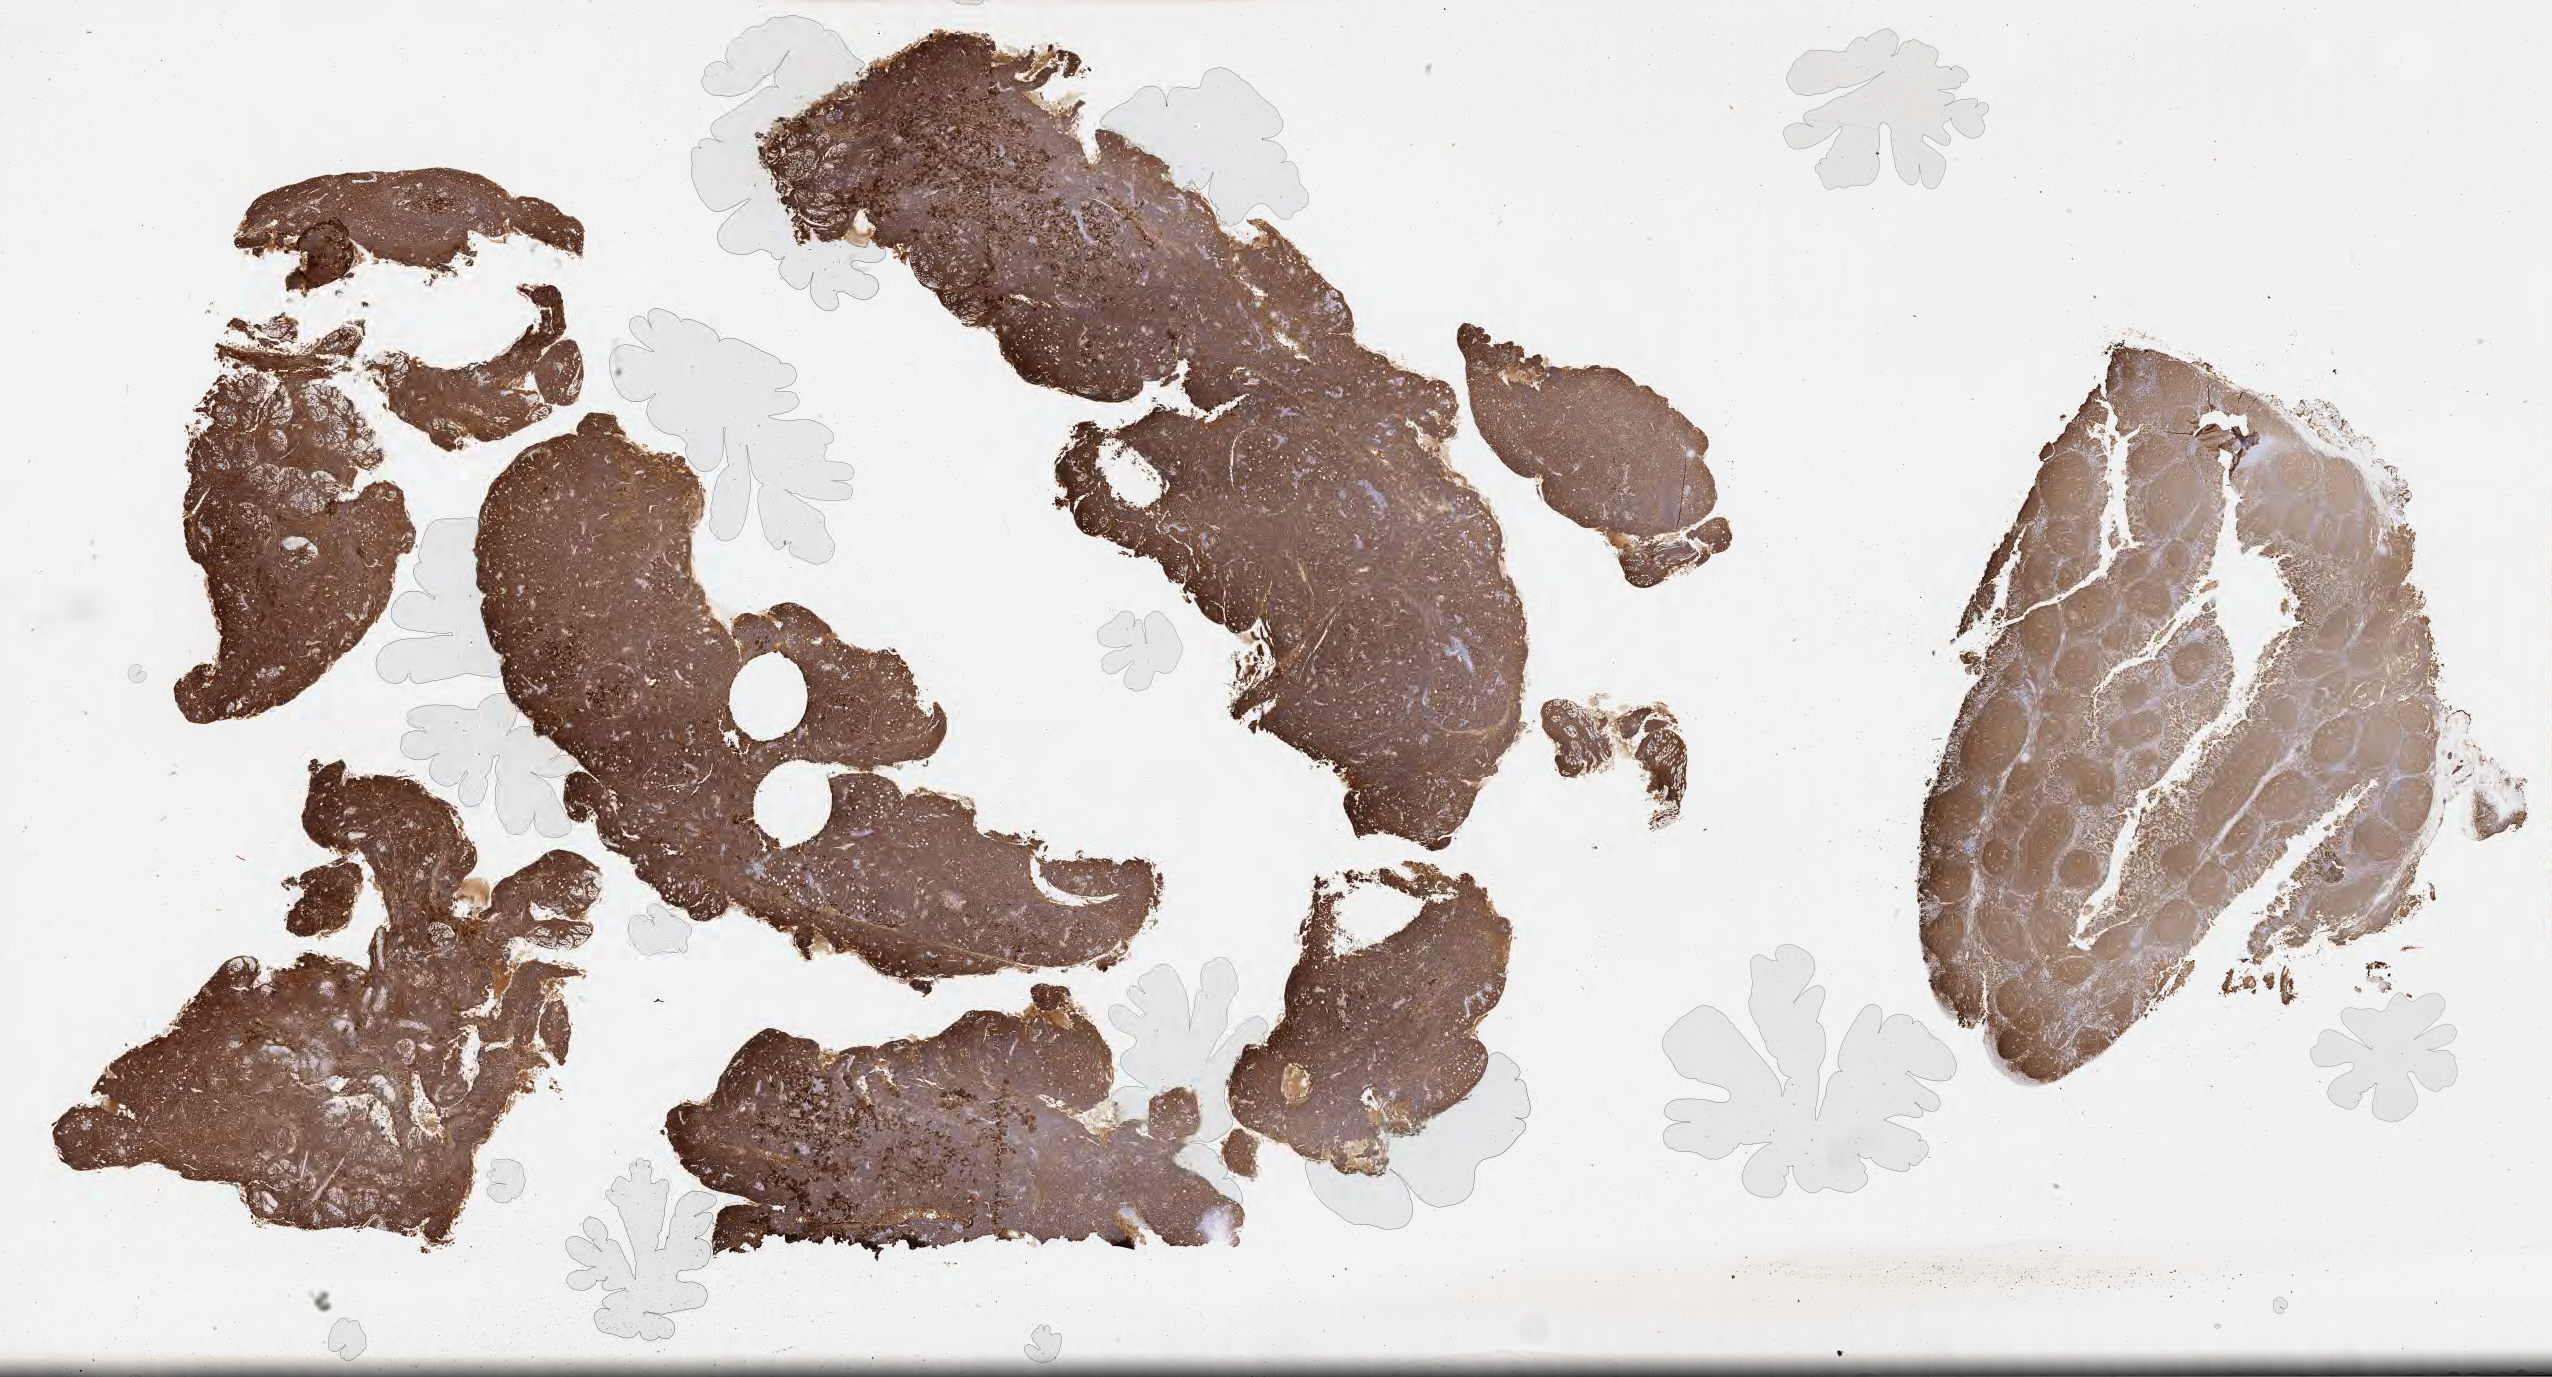
Whole-slide image, immunohistochemical stain for CD20, a low-resolution overview of the entire scanned area, about 41.3 x 22.3 mm; tumor tissue; anatomic site: cranium. Male, age 5 years at initial diagnosis.
Diagnosis: Burkitt lymphoma, NOS.